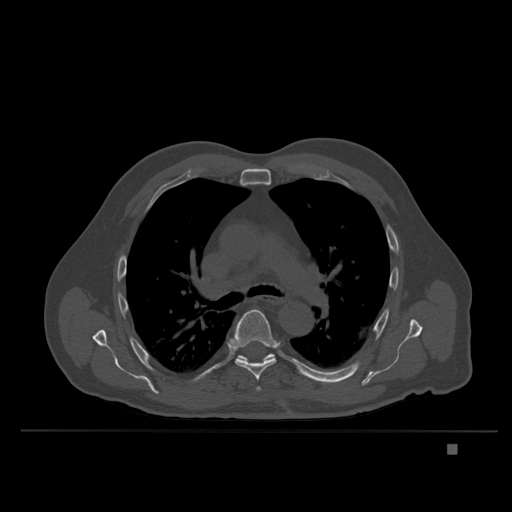
CT including the spine, one axial slice; position 257 of 435 along the scan axis; bone window (W 1800 / L 400 HU); 1.5 mm slice thickness; 512 × 512 image matrix, field of view 434 × 434 mm. Male patient, age 73 years. From the clinical record (not read from this slice): primary cancer: skin.
Outlined on this slice (semi-automatic segmentation, software-assisted and operator-edited):
- T5 vertebra: bounding box <256,387,261,391> (left, top, right, bottom; pixels)
- T6 vertebra: <228,310,277,381>
- T7 vertebra: <235,353,275,363>